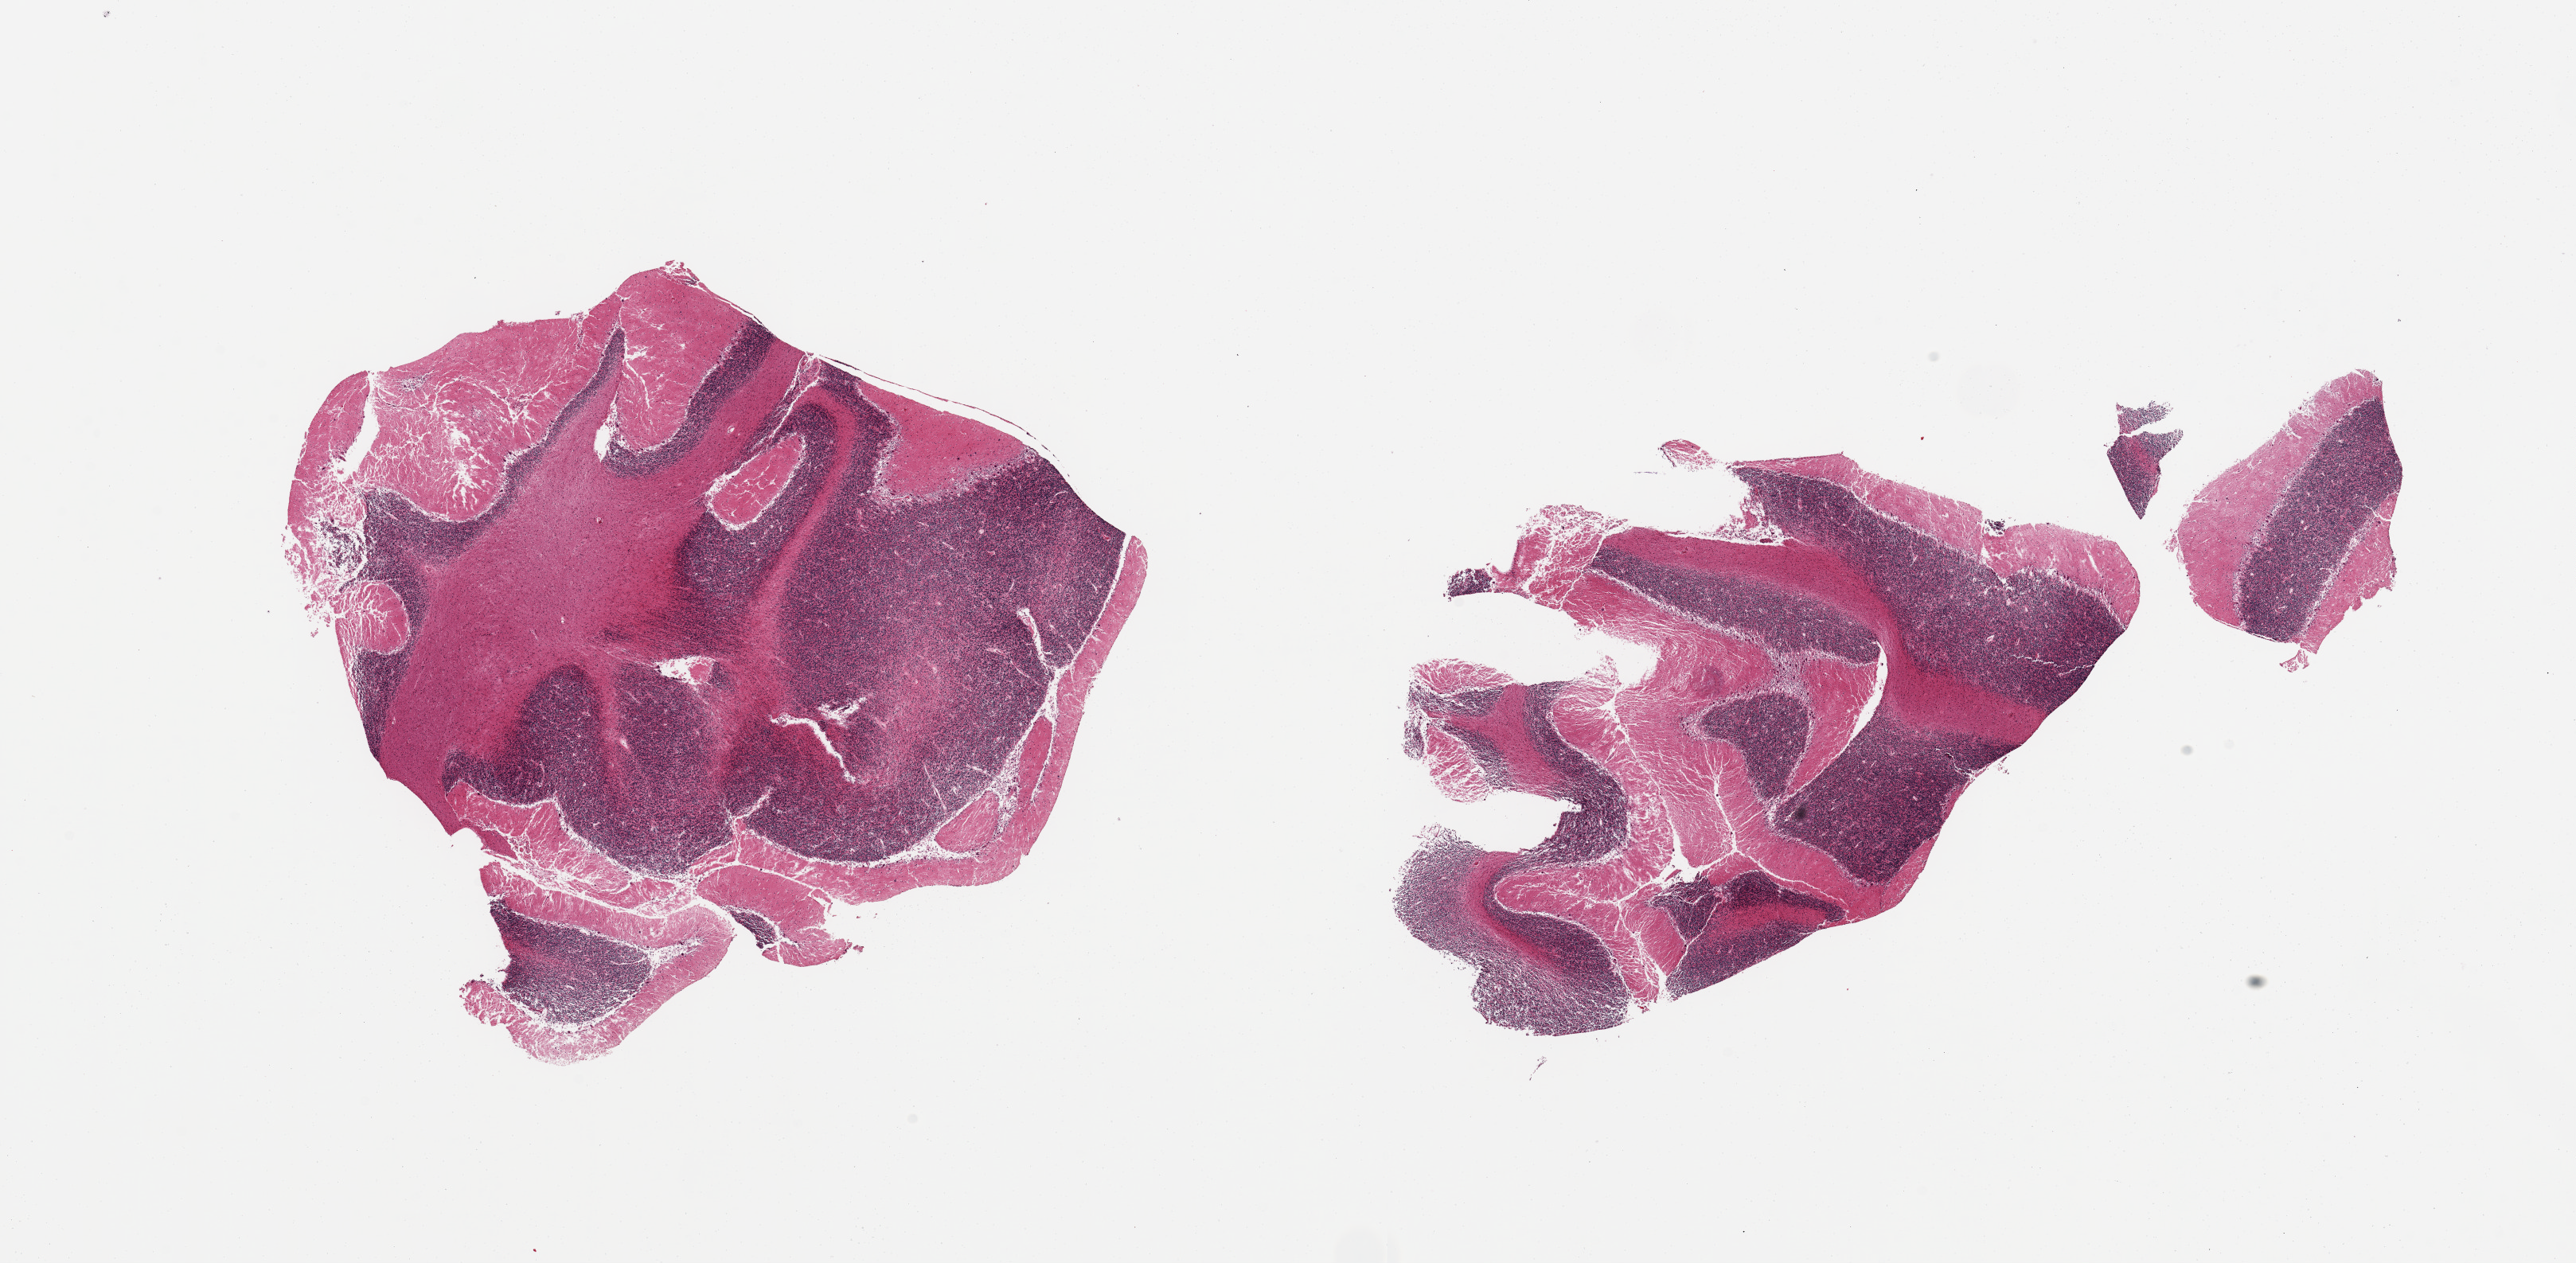
Hematoxylin and eosin (H&E) whole-slide image, whole scanned area (about 25.6 x 12.6 mm) shown as a low-resolution overview, PAXgene-fixed, paraffin-embedded tissue, section of cerebellum (target tissue), tissue donor sample. Donor sex: male.
Review note (as recorded): 2 pieces; moderately to severely autolyzed cerebellum, Purkinje cells with evidence of hypoxic damage.